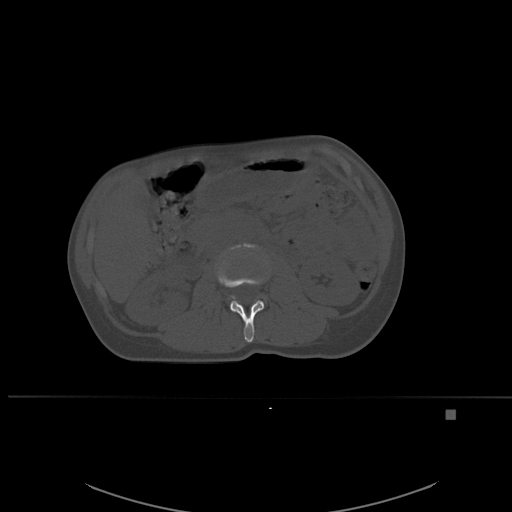
CT including the spine, one axial slice; position 228 of 537 along the scan axis; bone window (W 1800 / L 400 HU); 1.5 mm slice thickness; 512 × 512 image matrix. Female patient, age 45 years. Case-level facts recorded for this patient, not image findings: primary cancer: lung.
Annotated regions visible in this slice (semi-automatic segmentation, software-assisted and operator-edited):
- L2 vertebra: bounding box <217,261,264,342> (left, top, right, bottom; pixels)
- L3 vertebra: <221,243,256,297>